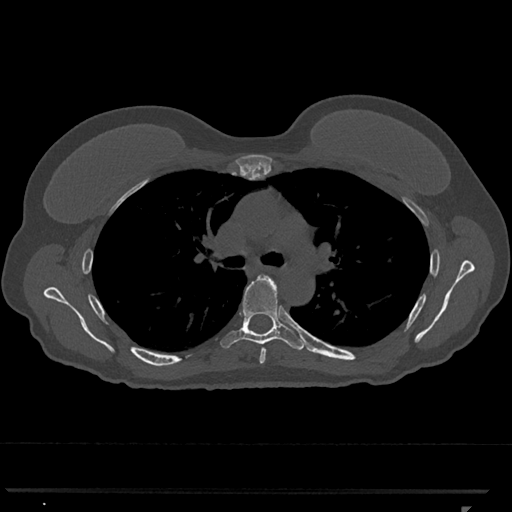
CT including the spine, one axial slice; slice 771 of 793 in the series (ordered by position); 120 kVp; bone window (W 1800 / L 400 HU); 512 × 512 image matrix. Patient: female, 62 years. From the clinical record (not read from this slice): primary cancer: renal.
Annotated regions visible in this slice (semi-automatically segmented with operator editing):
- T5 vertebra: box from (x=259, y=348) to (x=266, y=364) px
- T6 vertebra: (x=221, y=274)–(x=305, y=350)